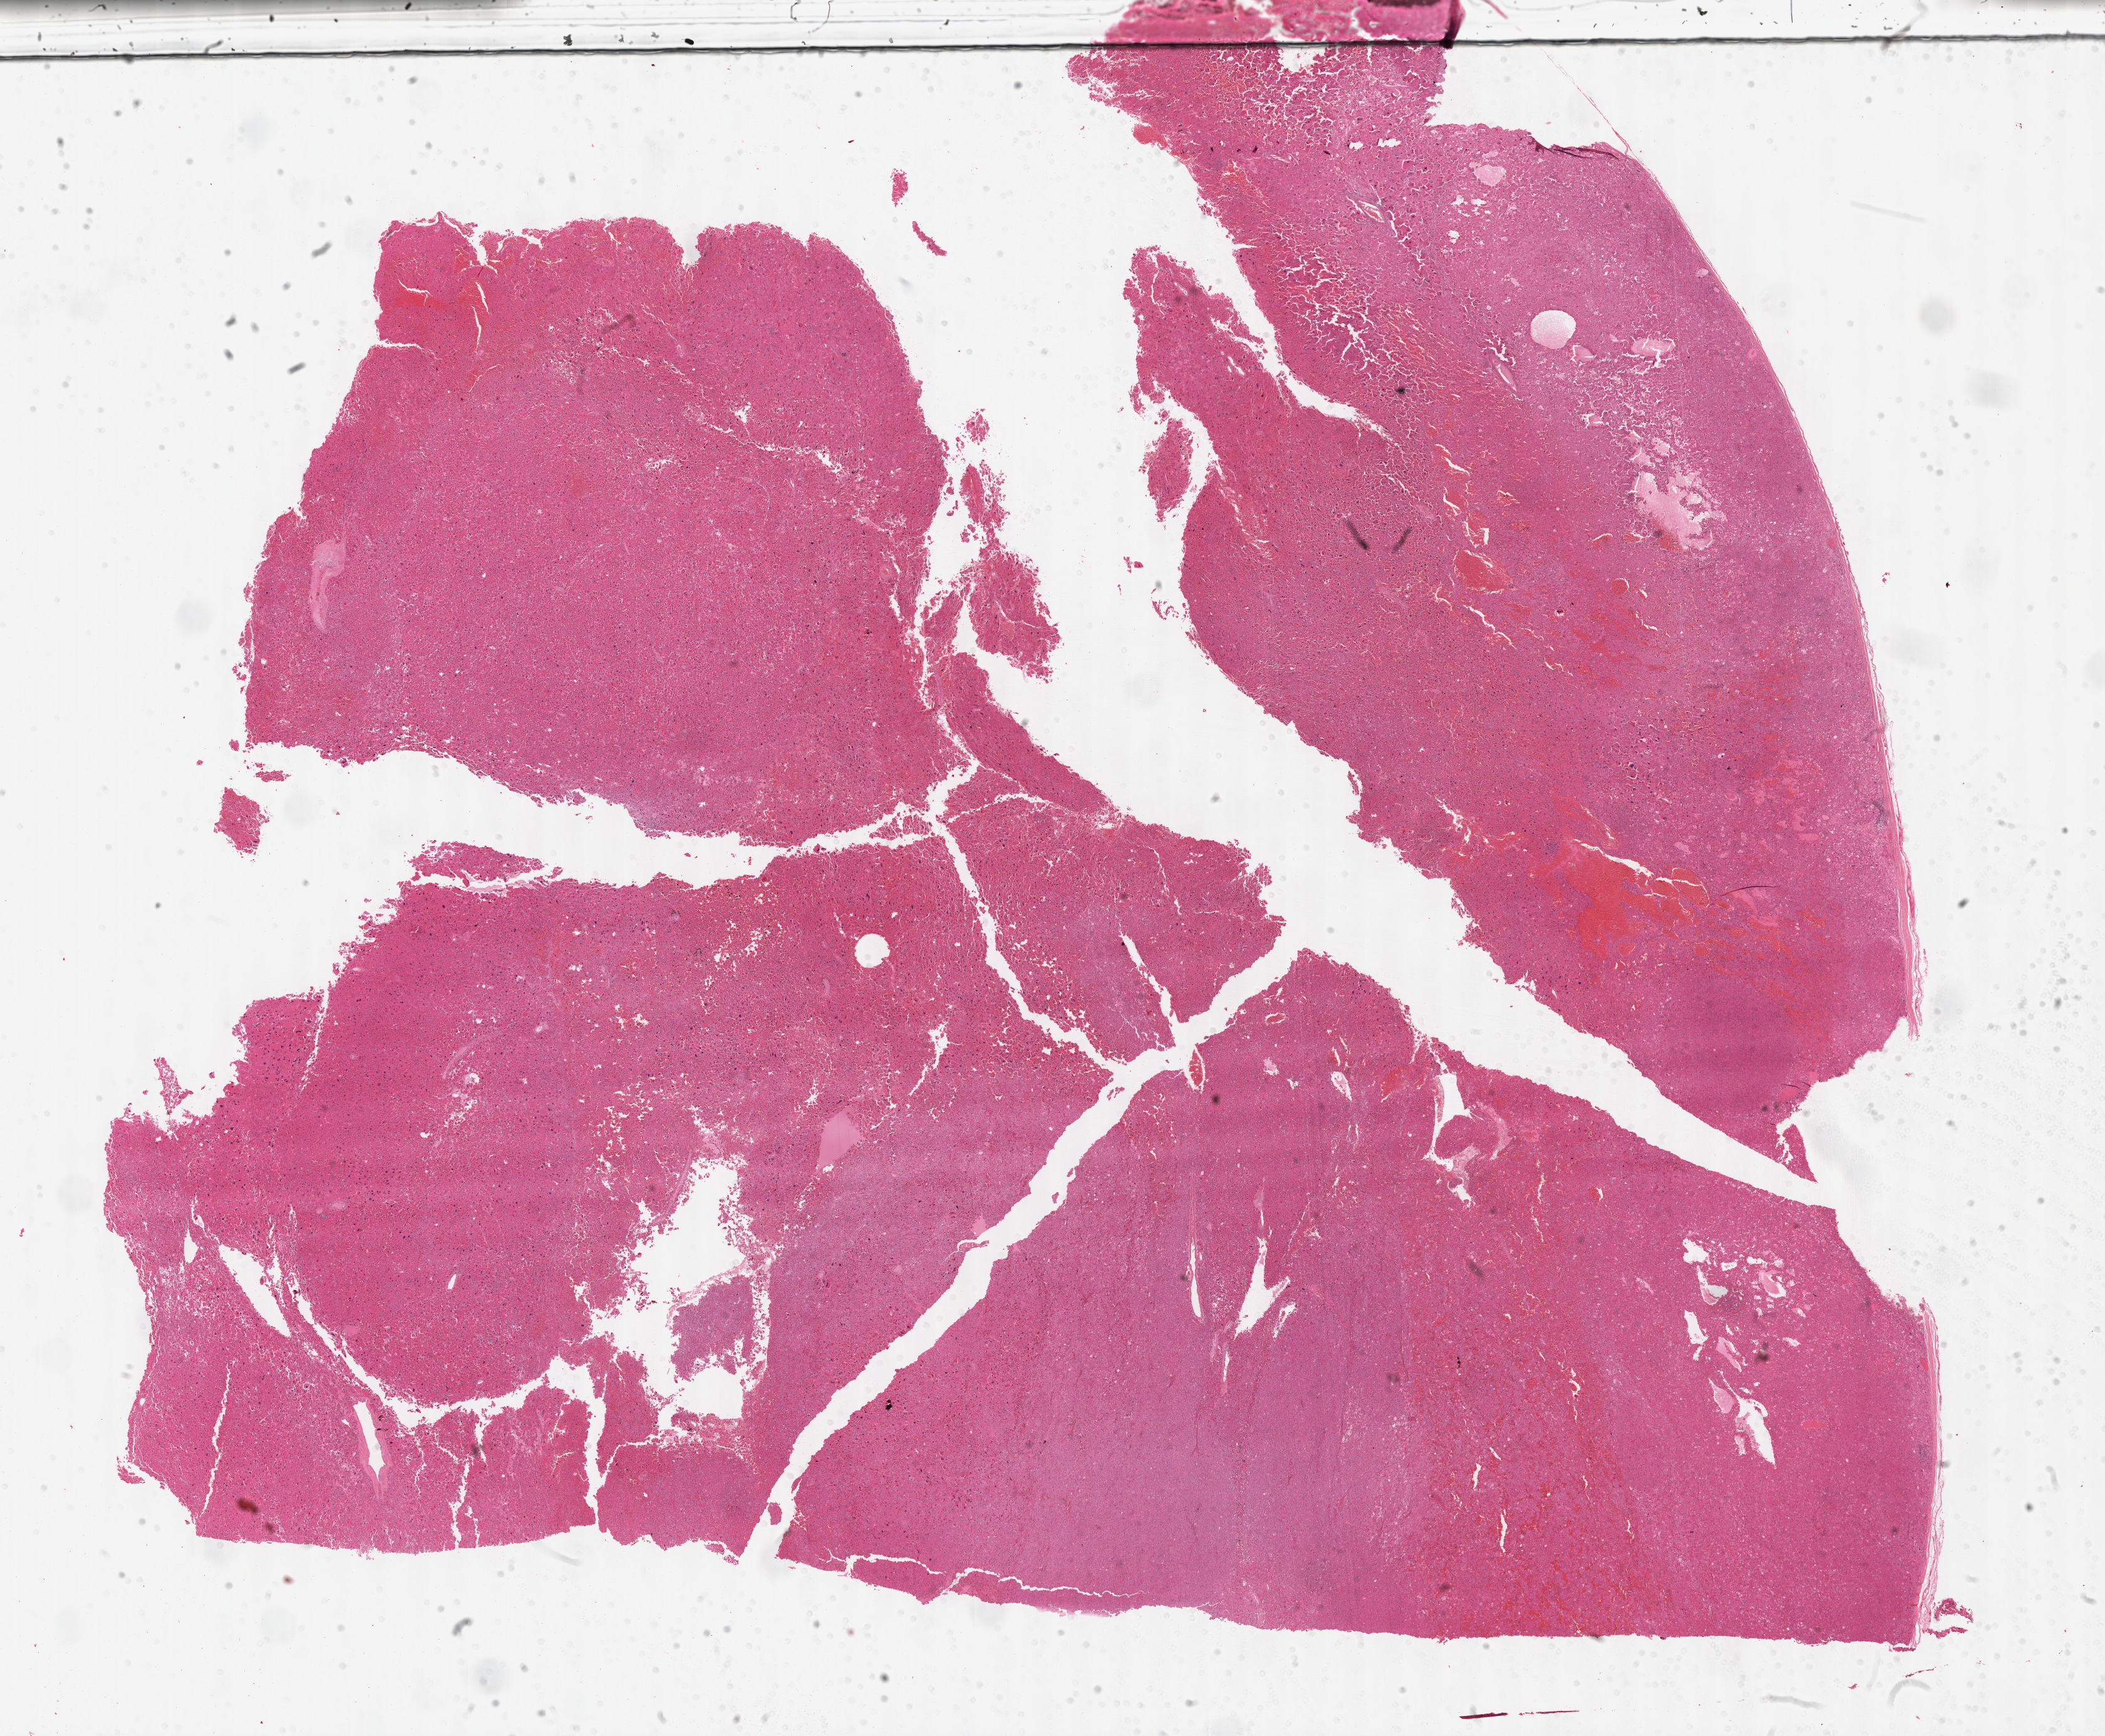
Hematoxylin and eosin (H&E) stained whole-slide image, a low-resolution overview of the entire scanned area, about 27.2 x 22.4 mm (slide scanned at 40x). Formalin-fixed paraffin-embedded (FFPE) diagnostic section. Sample: primary tumour, adrenal cortex. Female, age 57 years at initial diagnosis.
* laterality: left
* pathologic diagnosis: Adrenal cortical carcinoma (cortex of adrenal gland)